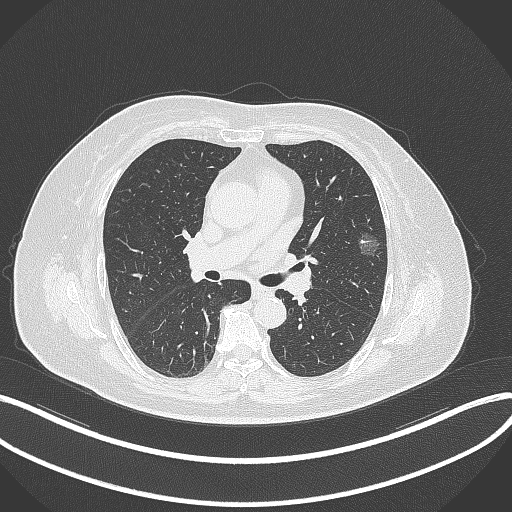
Chest CT, one axial slice; position 206 of 315 along the scan axis; reconstruction kernel B70f; lung window (W 1500 / L -600 HU); 1 mm slice thickness; 512 × 512 image matrix, field of view 400 × 400 mm. Patient: female, 76 years. Case-level facts recorded for this patient, not image findings: clinical TNM (as recorded): T1b N0 M0; histopathological grade: G1-2.
Structures marked on this image (rectangle marked by the reading radiologist):
- lung tumour (recorded histology: adenocarcinoma): bounding box (x1, y1, x2, y2) in pixels: (355, 228, 383, 261)